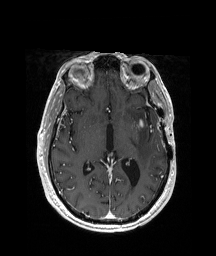
Brain MRI from a brain-tumour surgery series, one axial slice. Position 109 of 208 along the scan axis. T1-weighted post-contrast. 1 mm slice thickness. 216 × 256 image matrix, field of view 228 × 270 mm. Case-level facts recorded for this patient, not image findings: histopathology: Glioblastoma; WHO grade: 4; IDH mutation: no; tumour location: Left Anterior/Superior Temporal.
Structures marked on this image (expert manual segmentation):
- tumour: bounding box (x1, y1, x2, y2) in pixels: (139, 121, 143, 127)